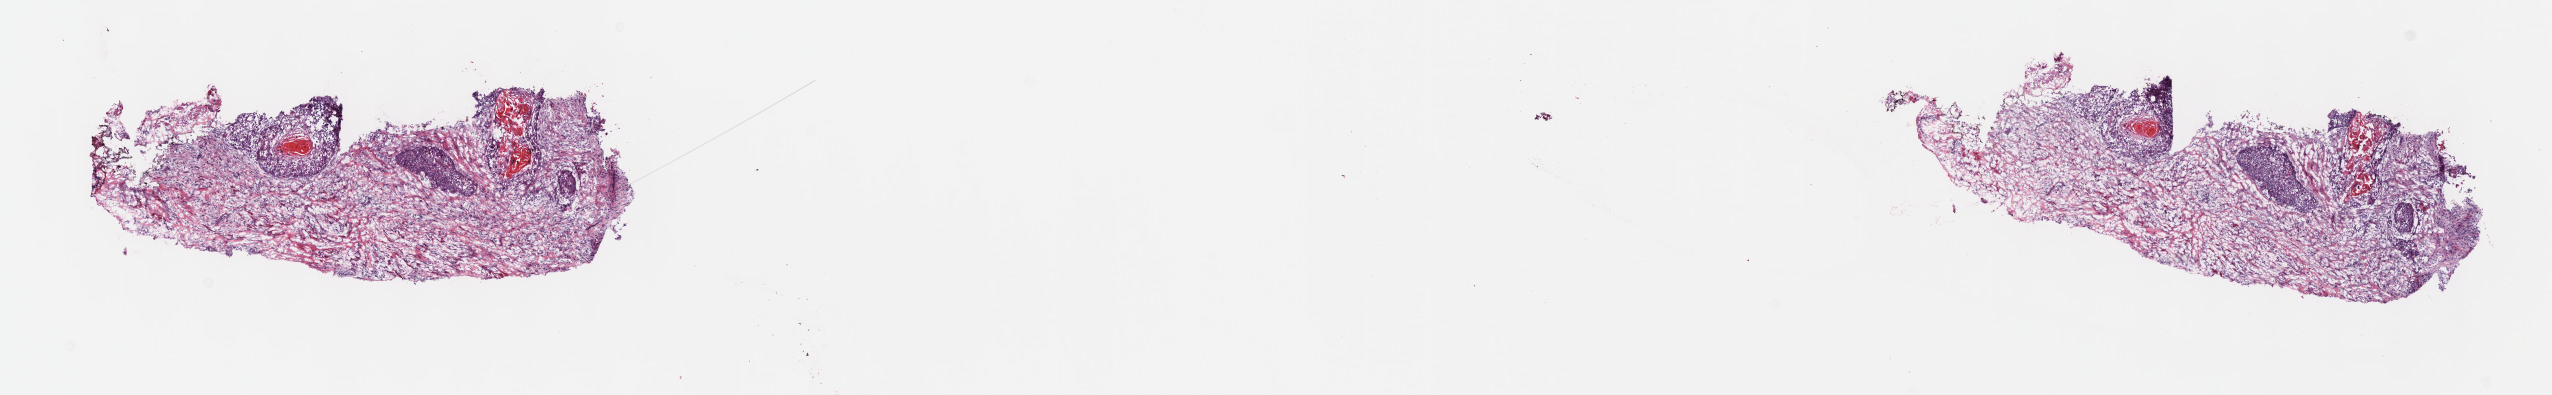
Whole-slide histology image, Hematoxylin and eosin (H&E) stained, shown as a low-resolution overview of the whole scanned area (about 20.6 x 3.2 mm, slide scanned at 40x). Frozen section. Primary tumour sample from the head and neck. Patient: male, age at initial diagnosis 59 years. Histologic grade: G1 (well differentiated). Composition of this section per pathologist review: tumour cells 25%, tumour nuclei 60%, normal cells 0%, stromal cells 75%, necrosis 0%. Inflammatory infiltration, as recorded: lymphocyte infiltration 4%, monocyte infiltration 6%, neutrophil infiltration 1%.
* AJCC pathologic stage: IVA
* diagnosis: Squamous cell carcinoma, NOS (larynx, NOS)